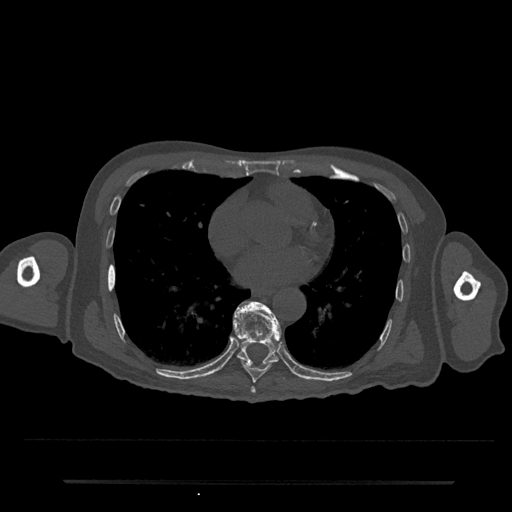
CT including the spine, one axial slice. Position 397 of 797 along the scan axis. Reconstruction kernel Br40s/3. 120 kVp. Bone window (W 1800 / L 400 HU). 0.5 mm slice thickness. 512 × 512 image matrix. Patient: male, 74 years. Case-level facts recorded for this patient, not image findings: primary cancer: prostate.
Structures marked on this image (semi-automatically segmented with operator editing):
- T7 vertebra: bounding box <250,387,256,394> (left, top, right, bottom; pixels)
- T8 vertebra: <243,362,272,383>
- T9 vertebra: <233,301,282,364>